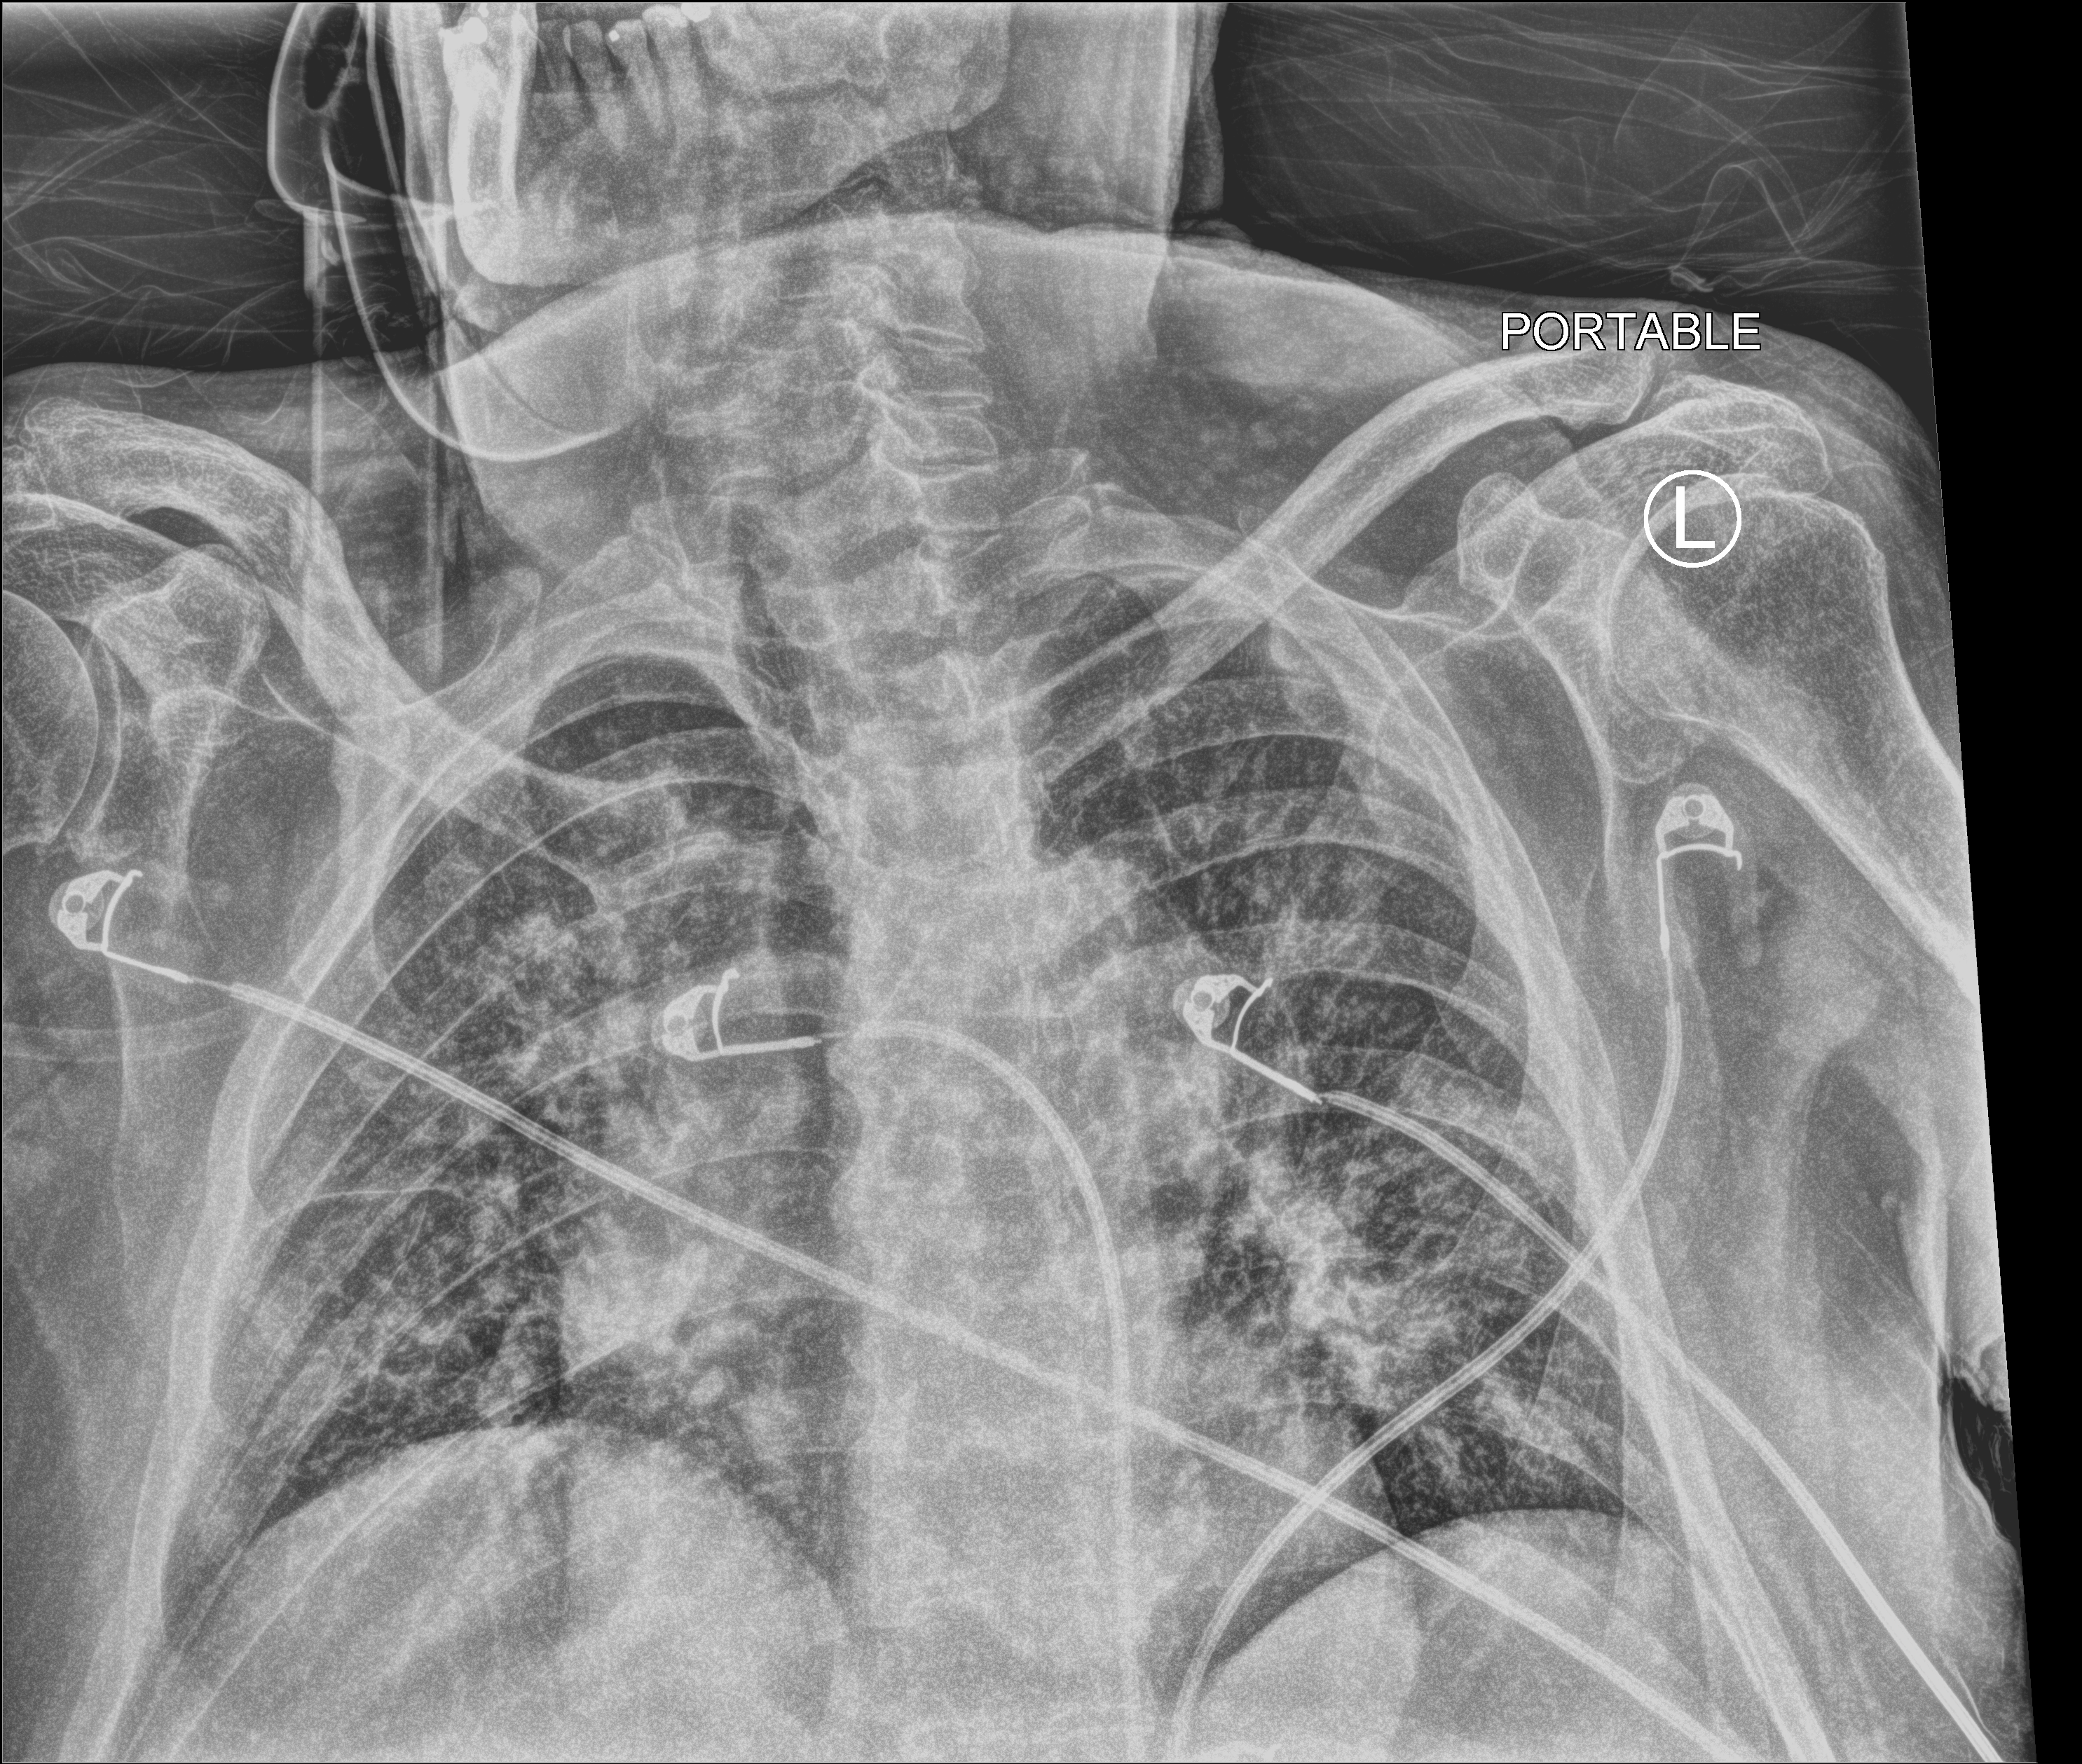
Portable chest radiograph; anteroposterior (AP) projection. Male patient hospitalised with COVID-19, age 75–90 years.
From the hospital-stay record, not from the radiograph (when in the stay this image was taken is not recorded): length of hospital stay: 5 days.